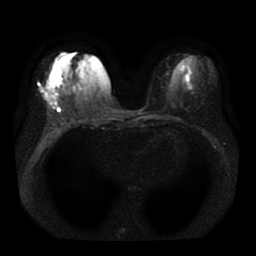
Breast MRI, one axial slice; diffusion-weighted series; image 2 of 4 stored at this slice position (different b-values; order by instance number); 1.5 T; 5 mm slice thickness; 256 × 256 image matrix, field of view 330 × 330 mm. Female patient.
Annotated regions visible in this slice (outlined manually by an expert reader):
- tumour on diffusion-weighted imaging: bounding box (x1, y1, x2, y2) in pixels: (42, 84, 56, 106)